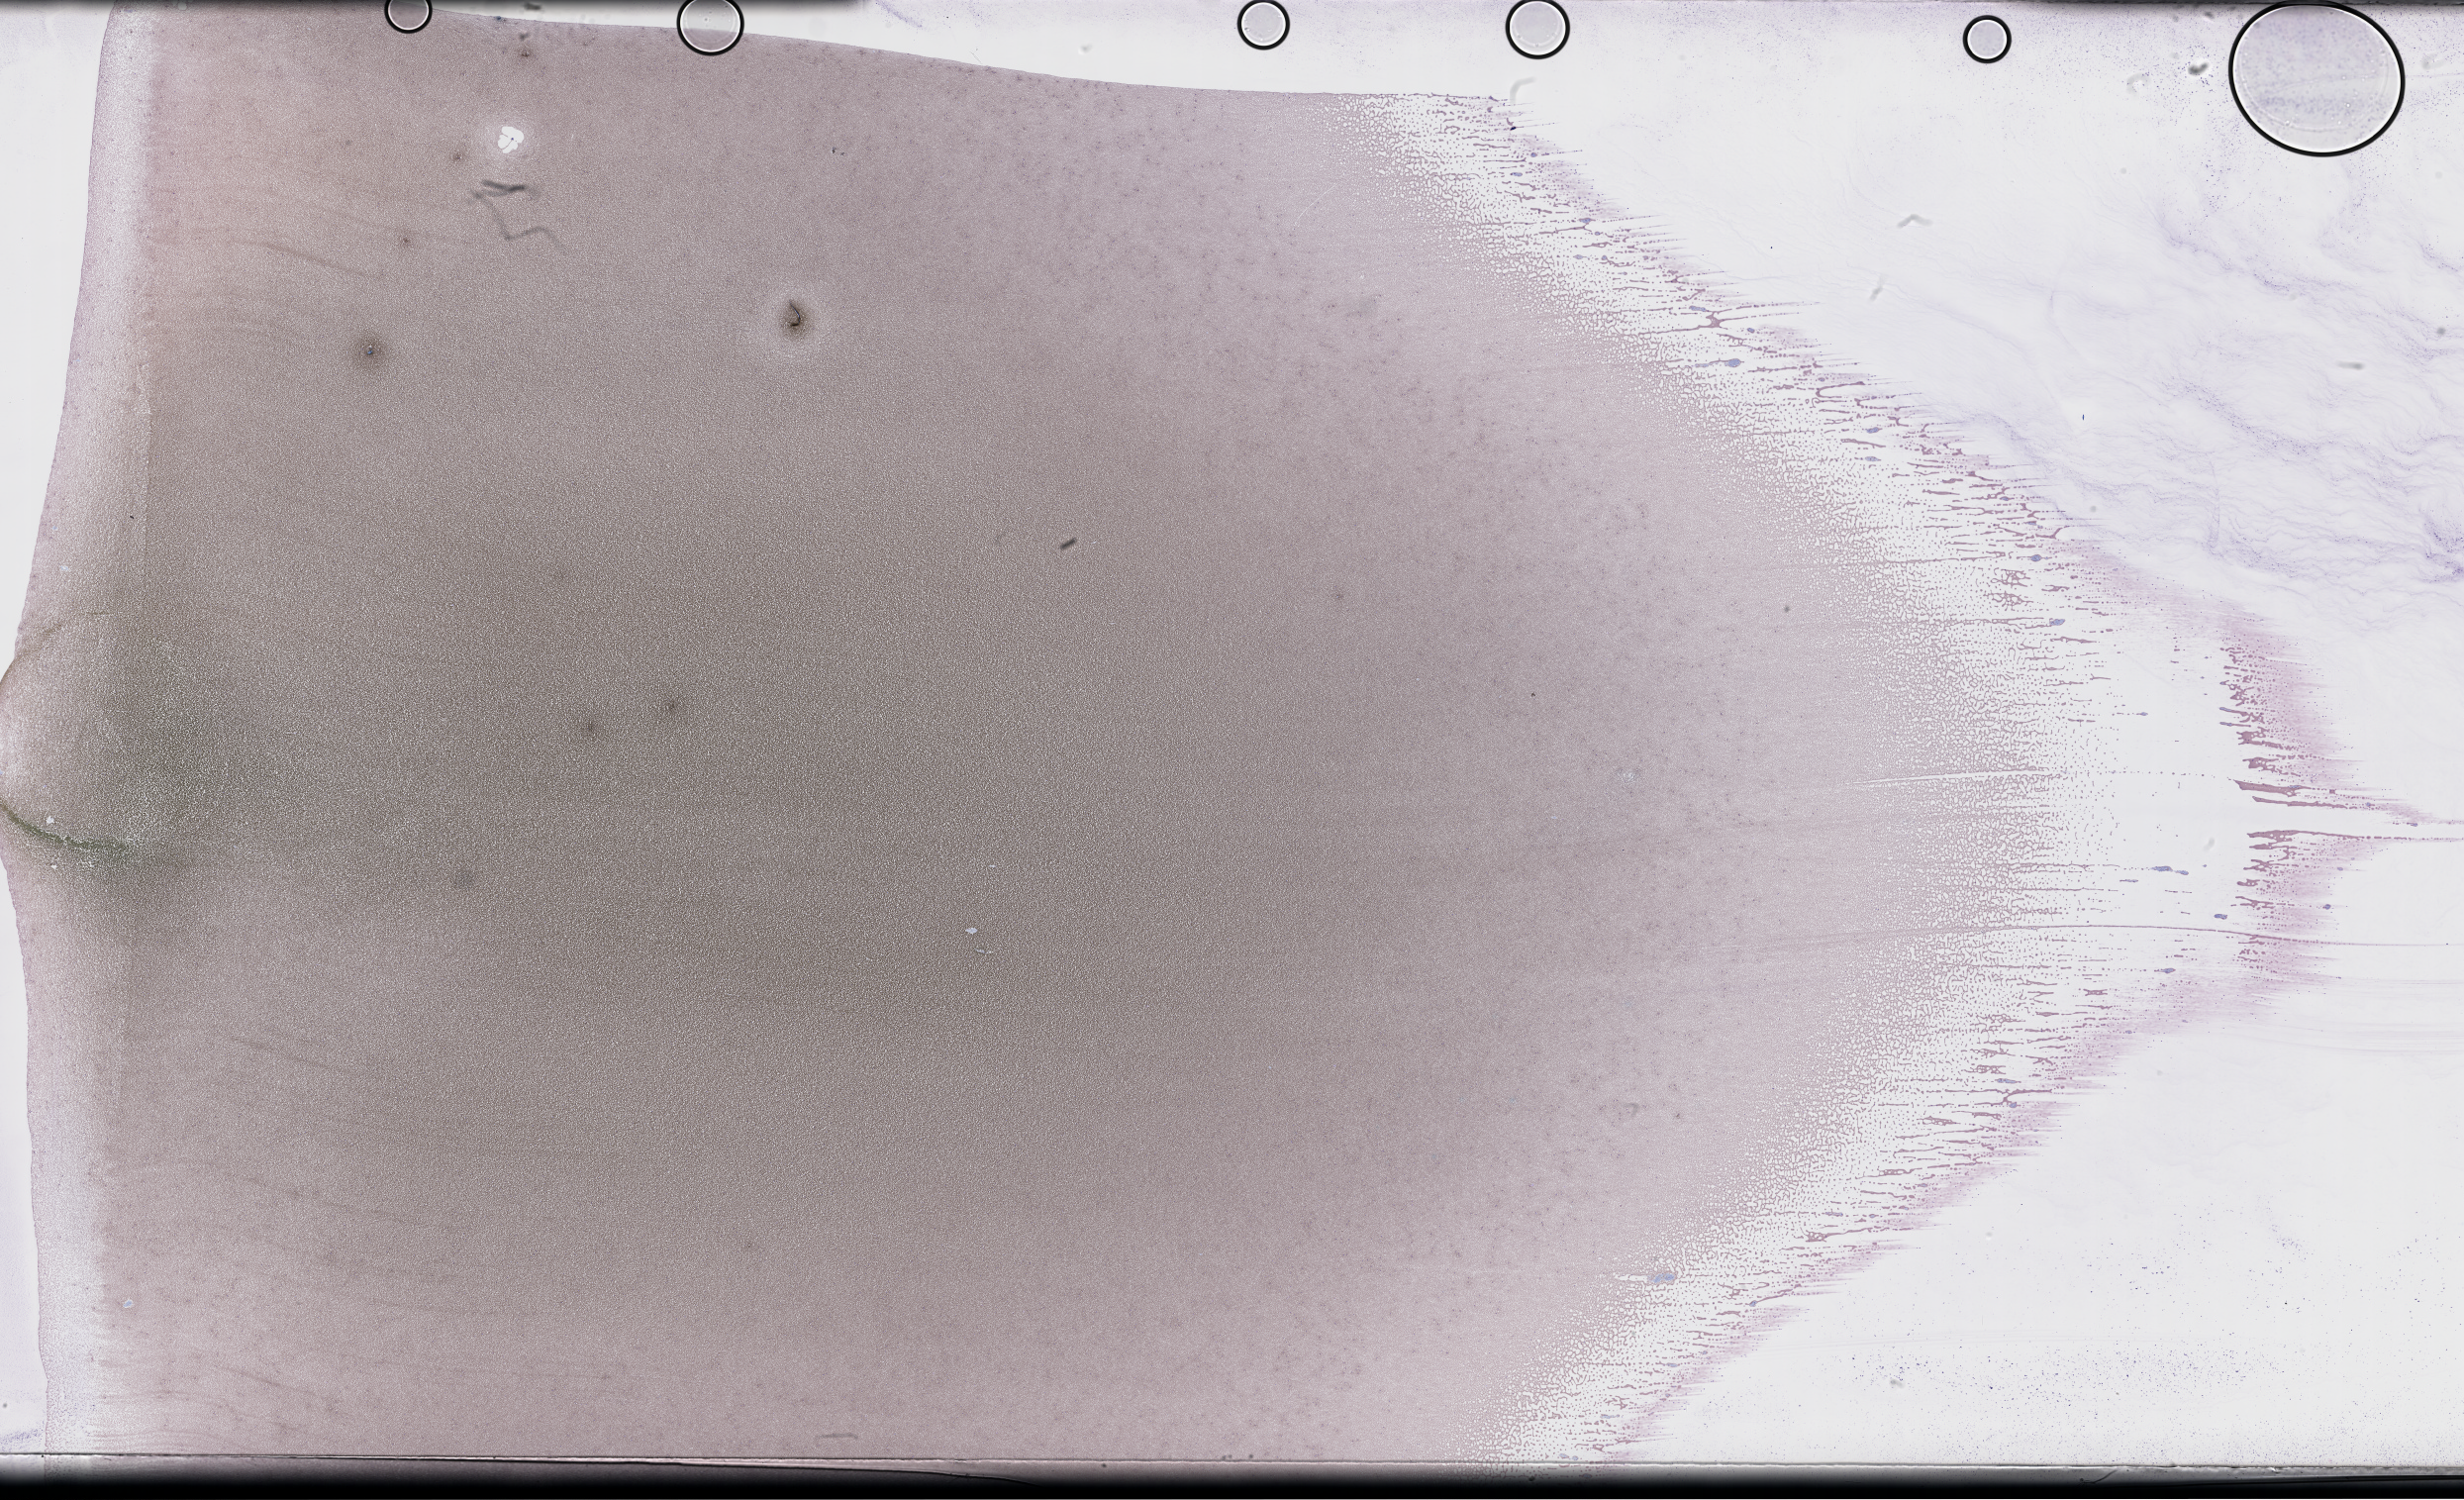
Wright–Giemsa-stained whole blood smear, whole-slide image — shown as a low-resolution overview of the whole scanned area (about 40.2 x 24.5 mm), smear from an EDTA sample, specimen time point: collected on treatment. Male patient.
* from a patient with: Plasma Cell Myeloma